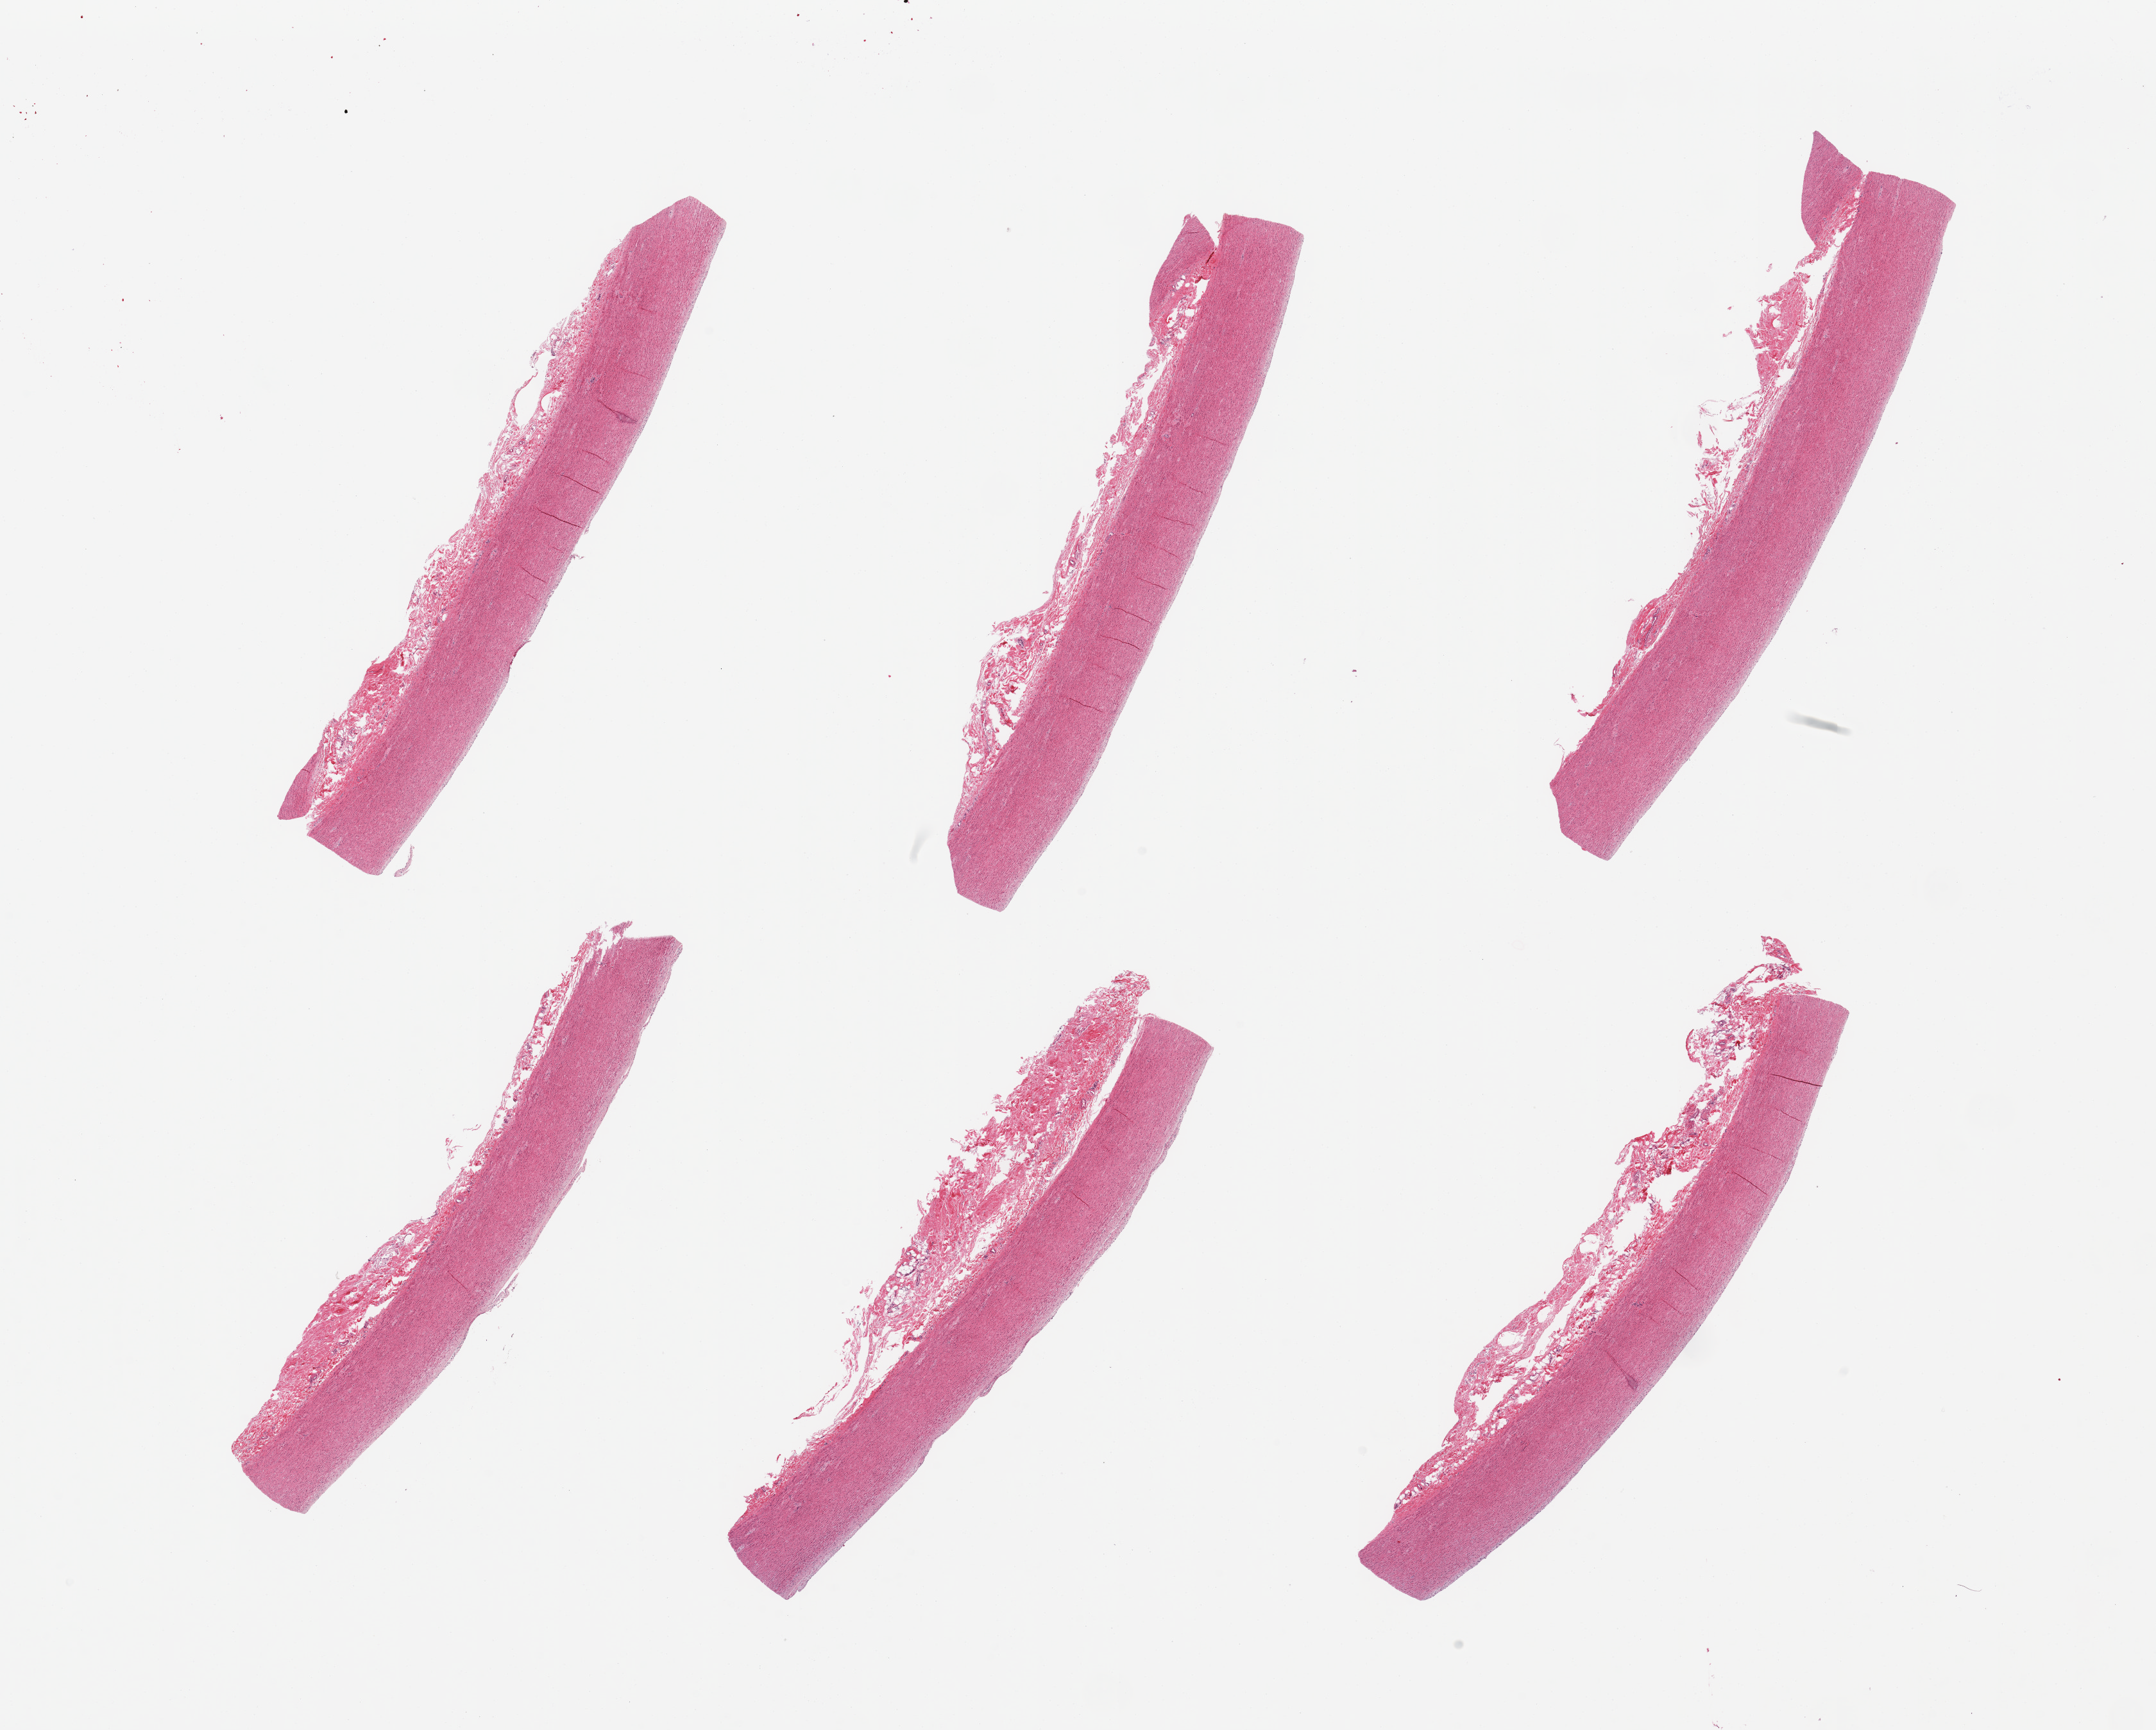
Whole-slide image, hematoxylin and eosin (H&E) stain — low-resolution overview of the scanned area, about 26.6 x 21.3 mm (slide scanned at 20x), PAXgene-fixed, paraffin-embedded tissue, target tissue: aorta, donor tissue sample. Donor sex: male.
Reviewer comment on this tissue sample: 6 pieces; no plaques; up to 1 mm adventitial stroma.